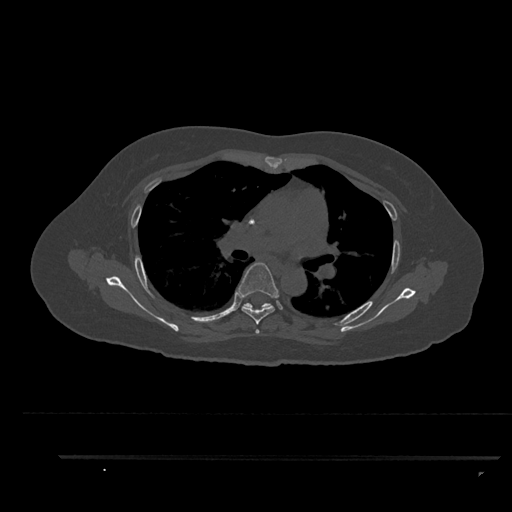
CT including the spine, one axial slice; position 592 of 797 along the scan axis; reconstruction kernel Br40s/3; 120 kVp; bone window (W 1800 / L 400 HU); 0.5 mm slice thickness; 512 × 512 image matrix, field of view 408 × 408 mm. Patient: female, 44 years. Case-level facts recorded for this patient, not image findings: primary cancer: renal; vertebrae with lytic lesions (as recorded): L1.
Annotated regions visible in this slice (semi-automatically segmented with operator editing):
- T4 vertebra: box from (x=255, y=329) to (x=260, y=334) px
- T5 vertebra: (x=238, y=262)–(x=279, y=325)
- T6 vertebra: (x=242, y=303)–(x=273, y=310)